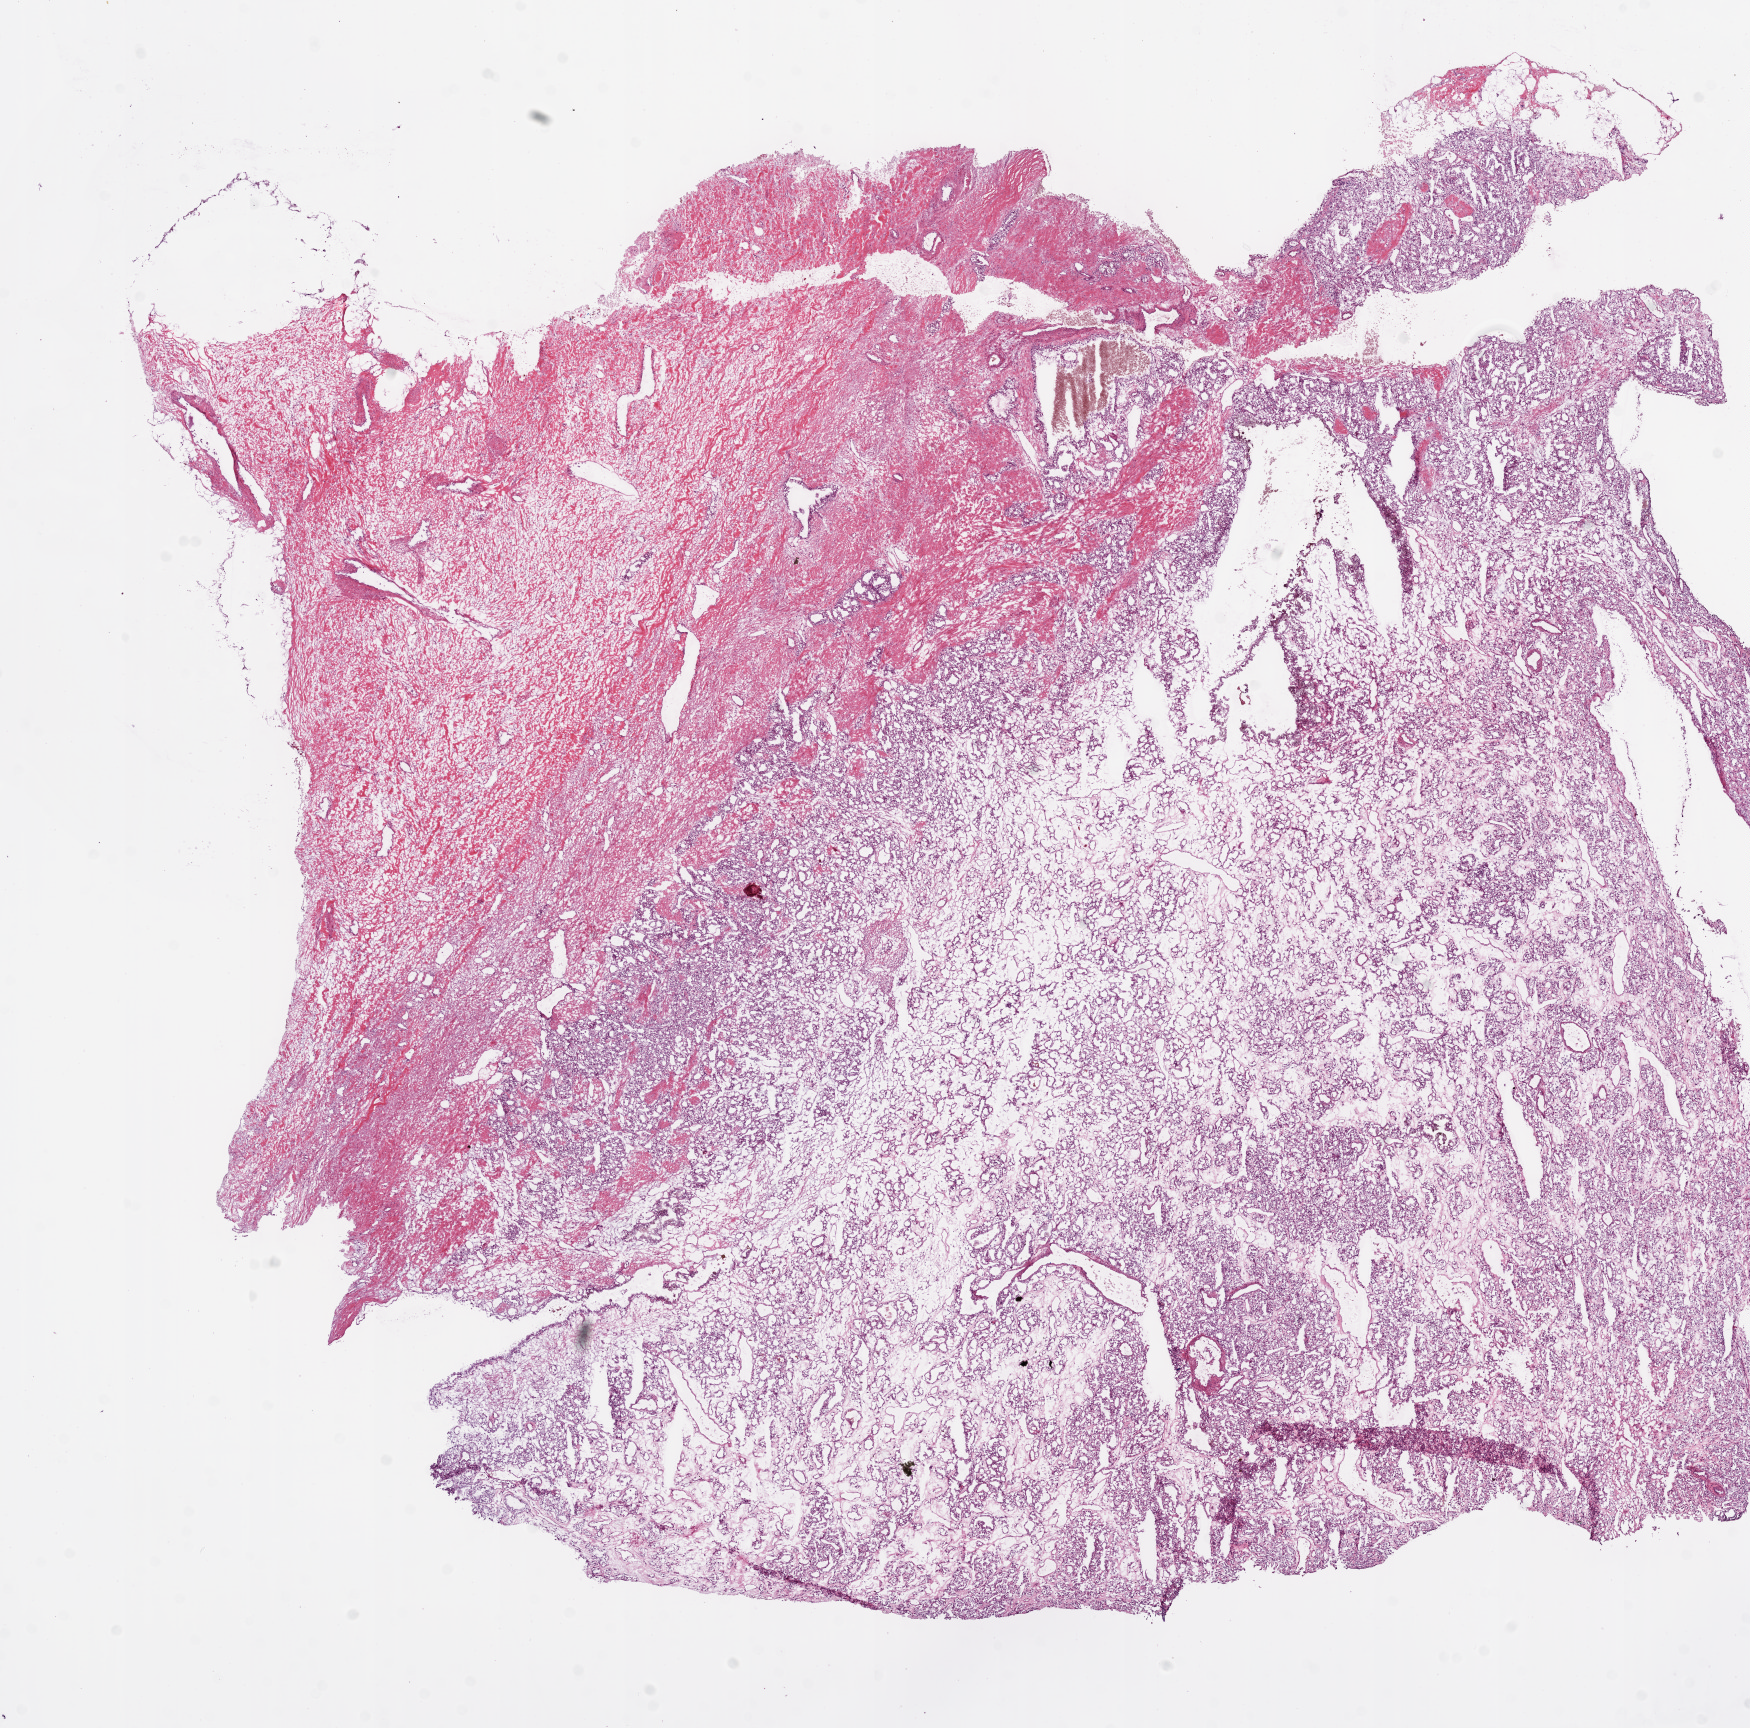
H&E-stained whole-slide image, low-resolution overview of the scanned area, about 14.0 x 13.9 mm (acquisition: 20x scan). Frozen section. Kidney, primary tumour sample. Male, age 63 years at initial diagnosis. Histologic grade: G2 (moderately differentiated). Composition of this section per pathologist review: tumour cells 60%, tumour nuclei 80%, normal cells 0%, stromal cells 40%, necrosis 0%.
• histologic diagnosis: Clear cell adenocarcinoma, NOS
• AJCC pathologic stage: I